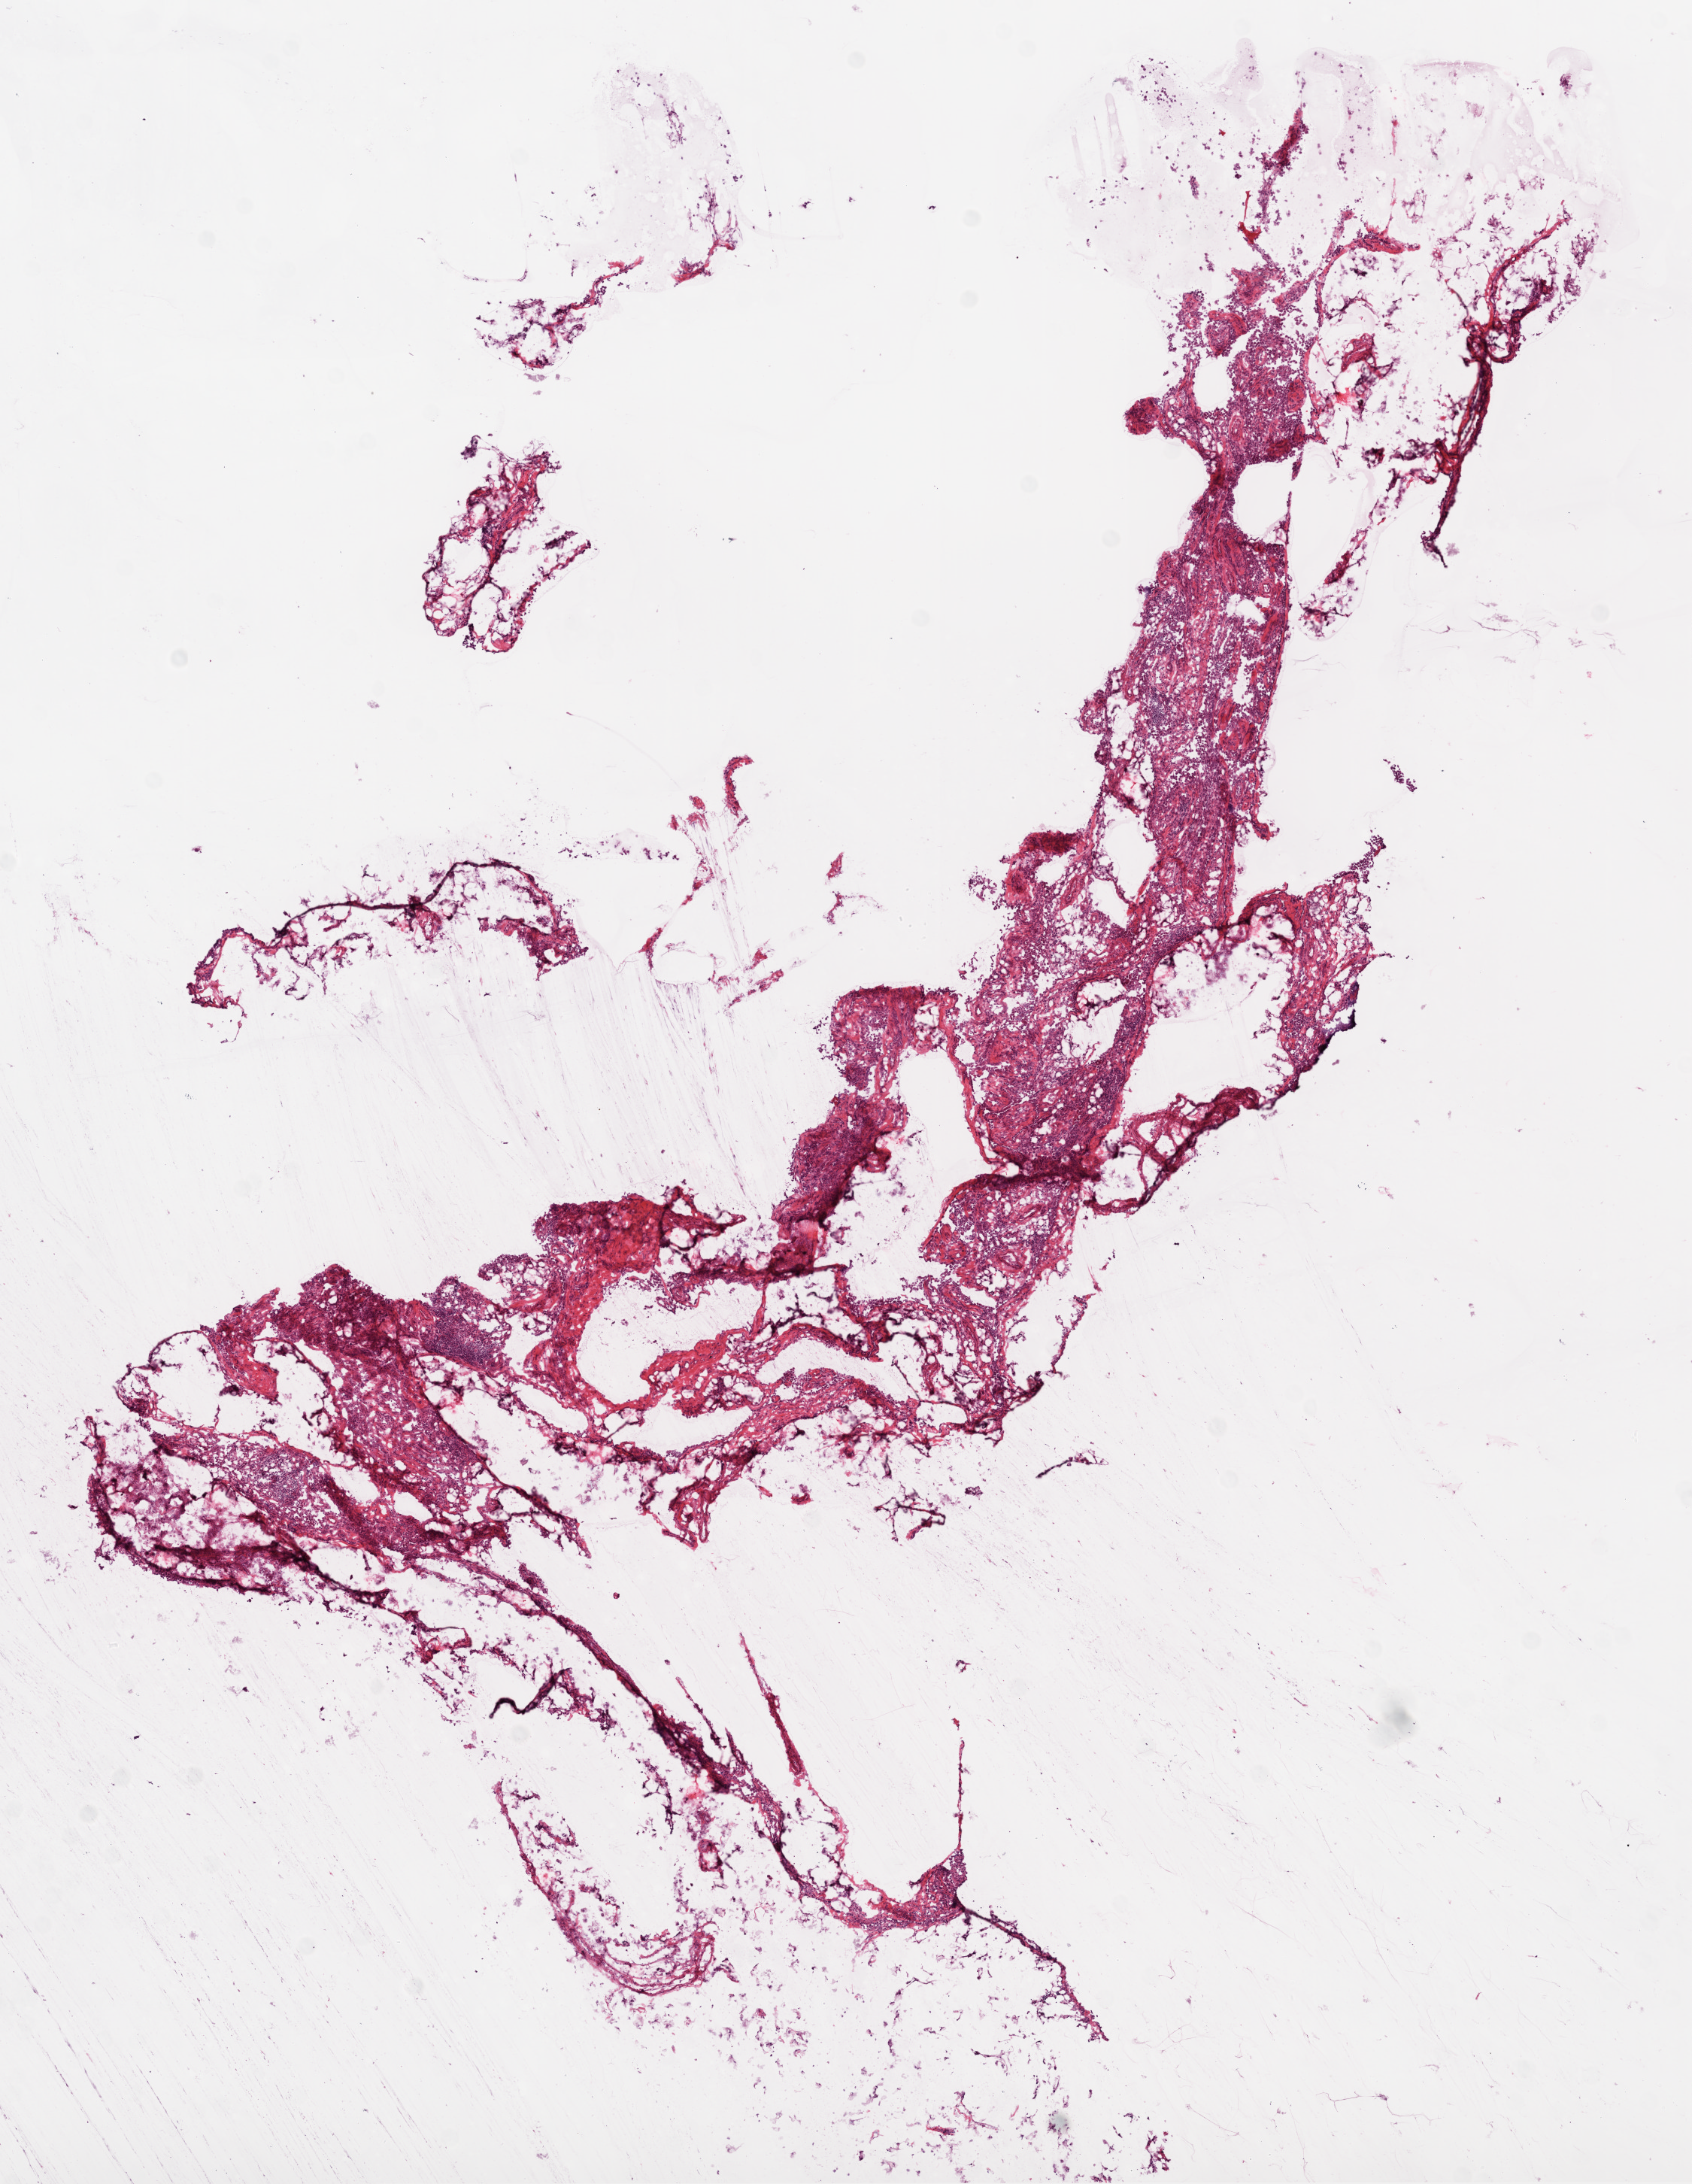
Digitized Hematoxylin and eosin (H&E) stained tissue section (whole slide) — shown as a low-resolution overview of the whole scanned area (about 9.0 x 11.7 mm). Frozen section. Sample: solid tissue normal (non-tumour tissue), ovary. Patient: female, age at initial diagnosis 69 years.
This section: solid tissue normal sample (biorepository sample class). Patient diagnosis: Serous cystadenocarcinoma, NOS.